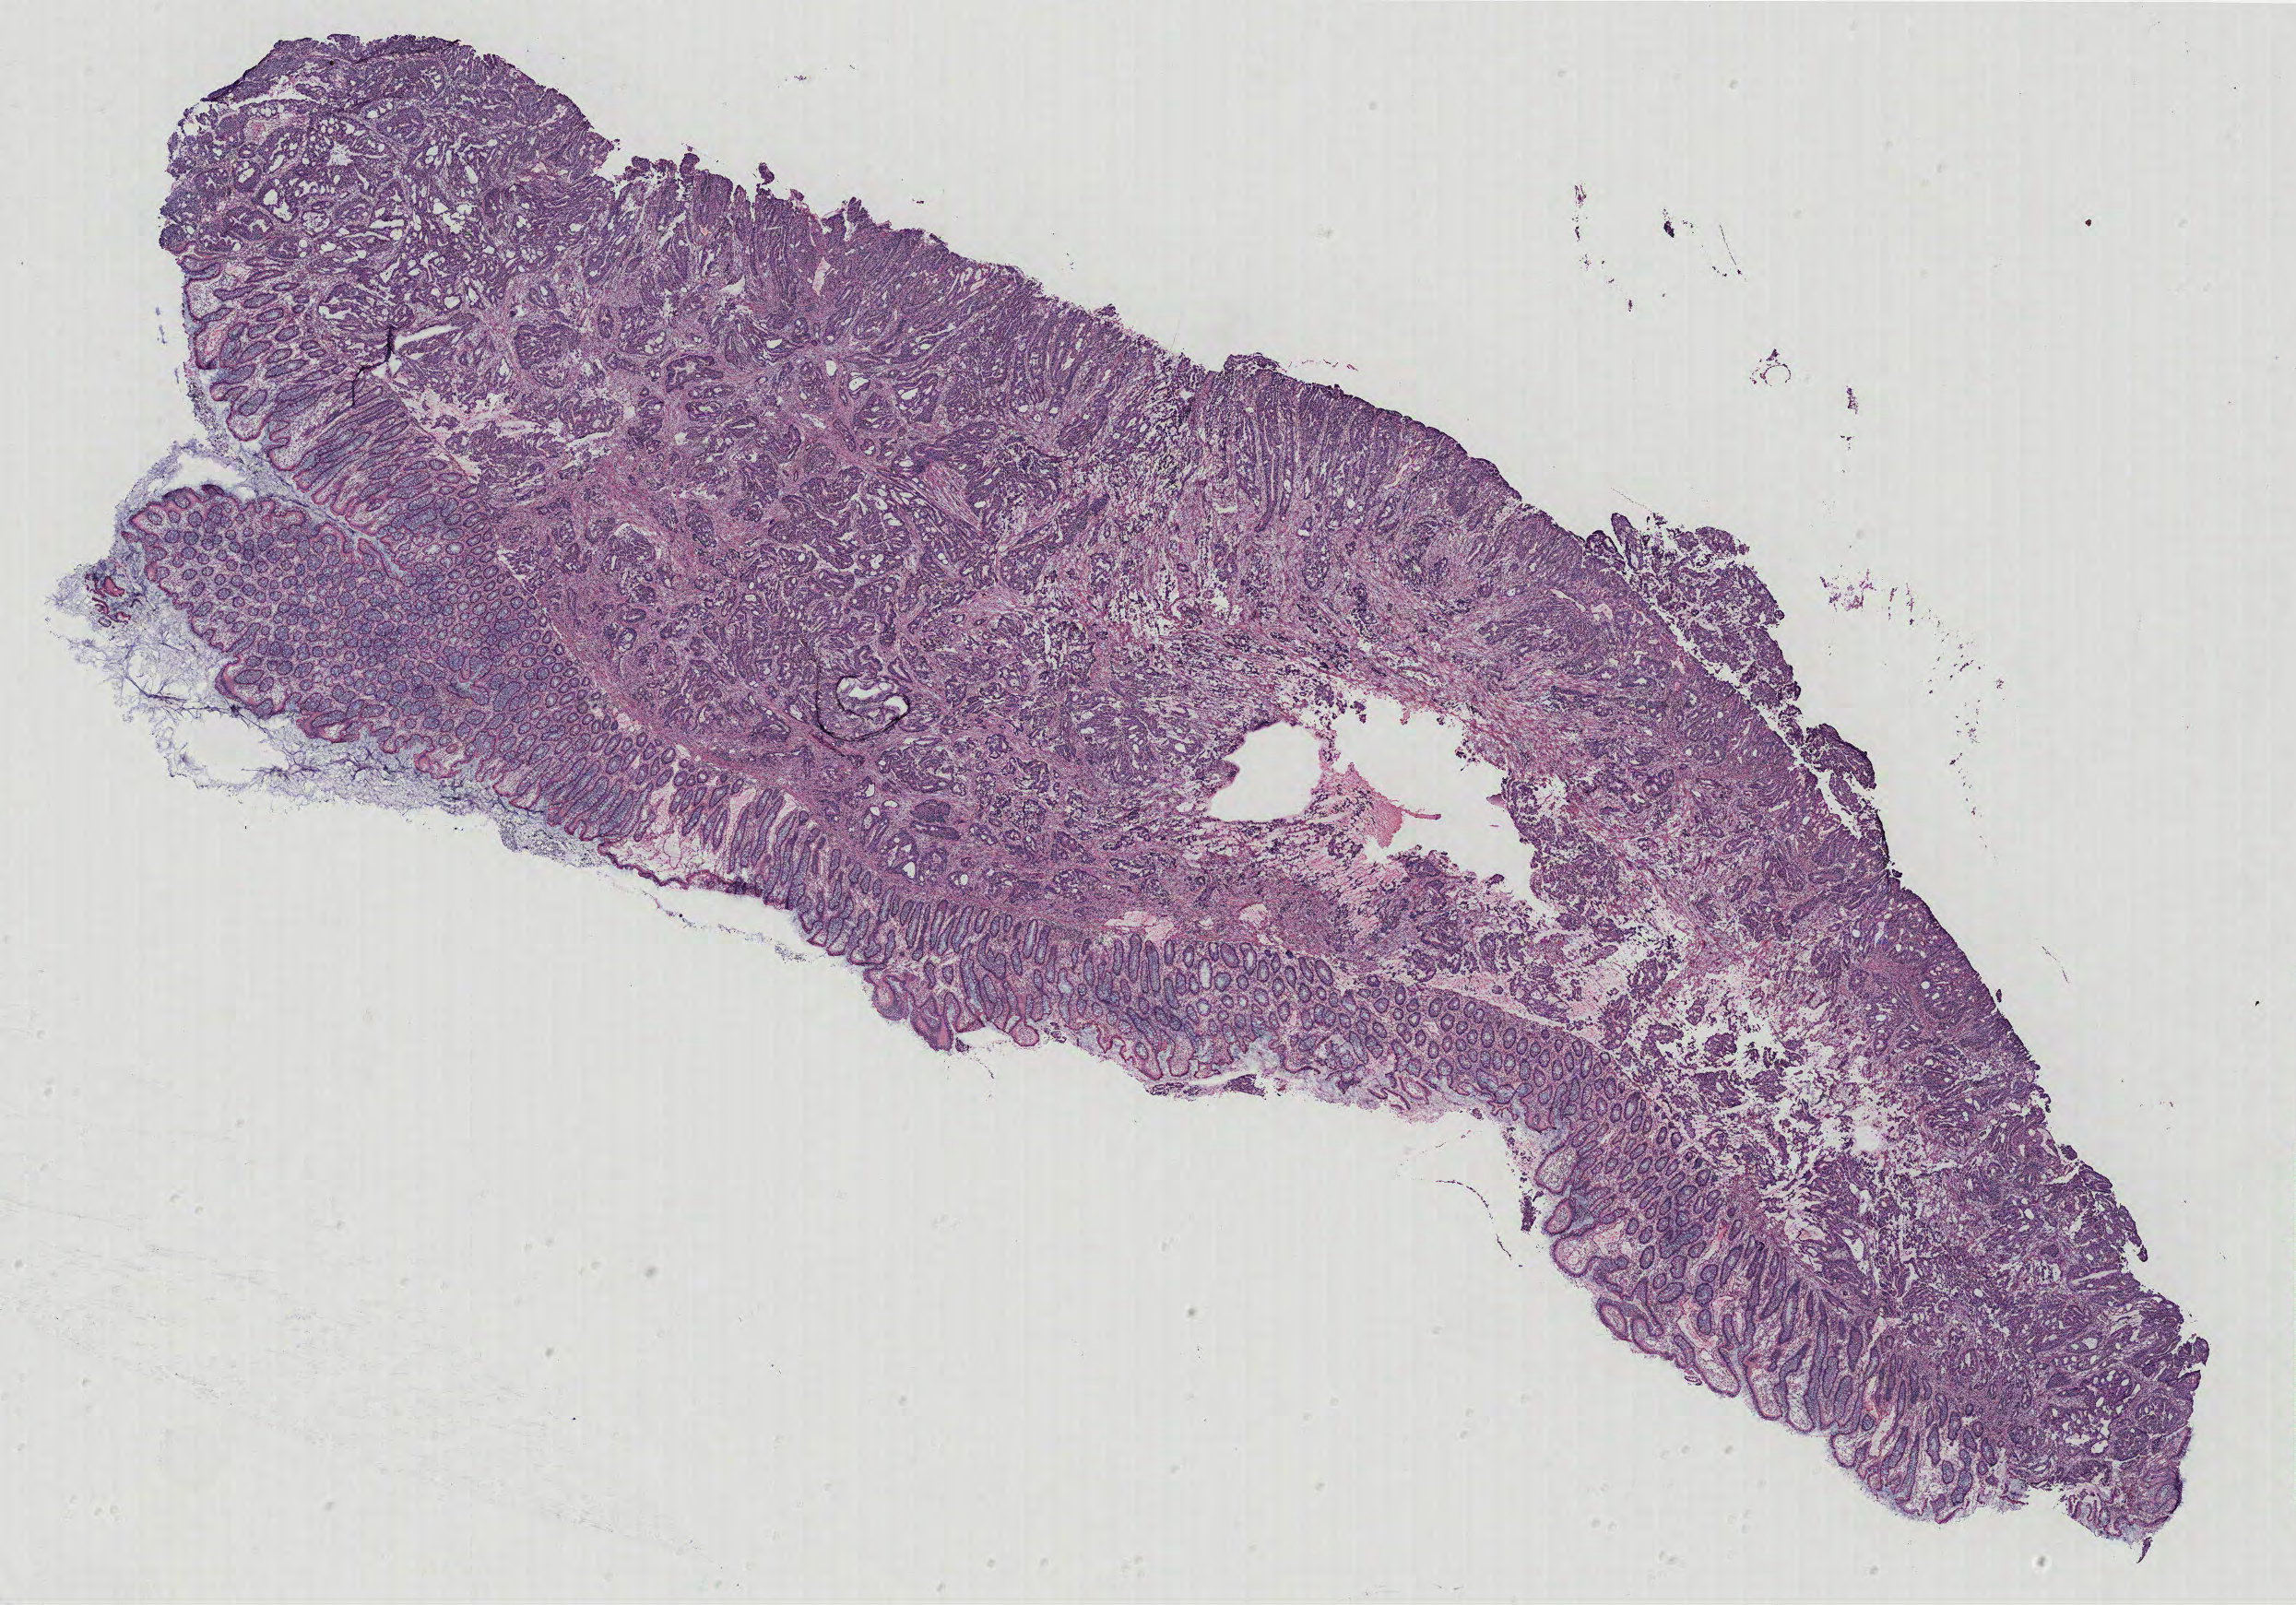
Whole-slide histology image, H&E, whole scanned area (about 19.9 x 13.9 mm, acquisition: 40x scan) shown as a low-resolution overview. Colon, normal (non-tumour) tissue. 63-year-old female patient.
This section: normal (non-tumour) tissue from the same patient. Patient diagnosis: Adenocarcinoma, NOS.